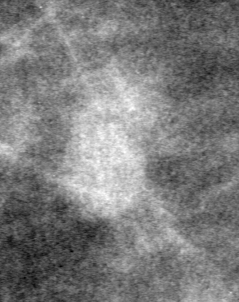
Region of interest cut from a scanned film mammogram (one marked finding); left breast; CC view.
Mass, shape lobulated, margins ill defined; BI-RADS assessment category 4; pathology (as recorded): benign.